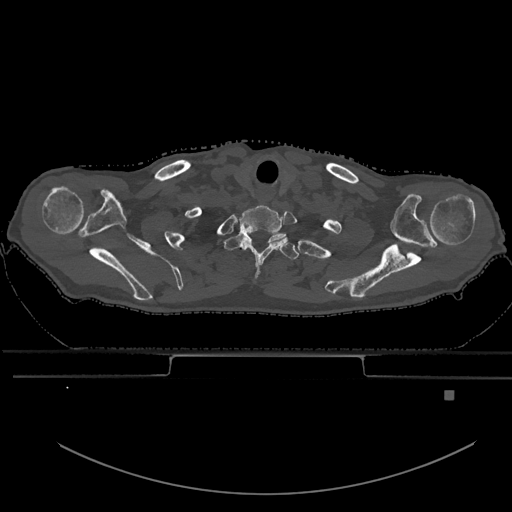
CT including the spine, one axial slice. Position 554 of 969 along the scan axis. Bone window (W 1800 / L 400 HU). 512 × 512 image matrix, field of view 456 × 456 mm. Patient: male, 82 years. Case-level facts recorded for this patient, not image findings: primary cancer: prostate.
Structures marked on this image (semi-automatically segmented with operator editing):
- T1 vertebra: bounding box <224,232,299,260> (left, top, right, bottom; pixels)